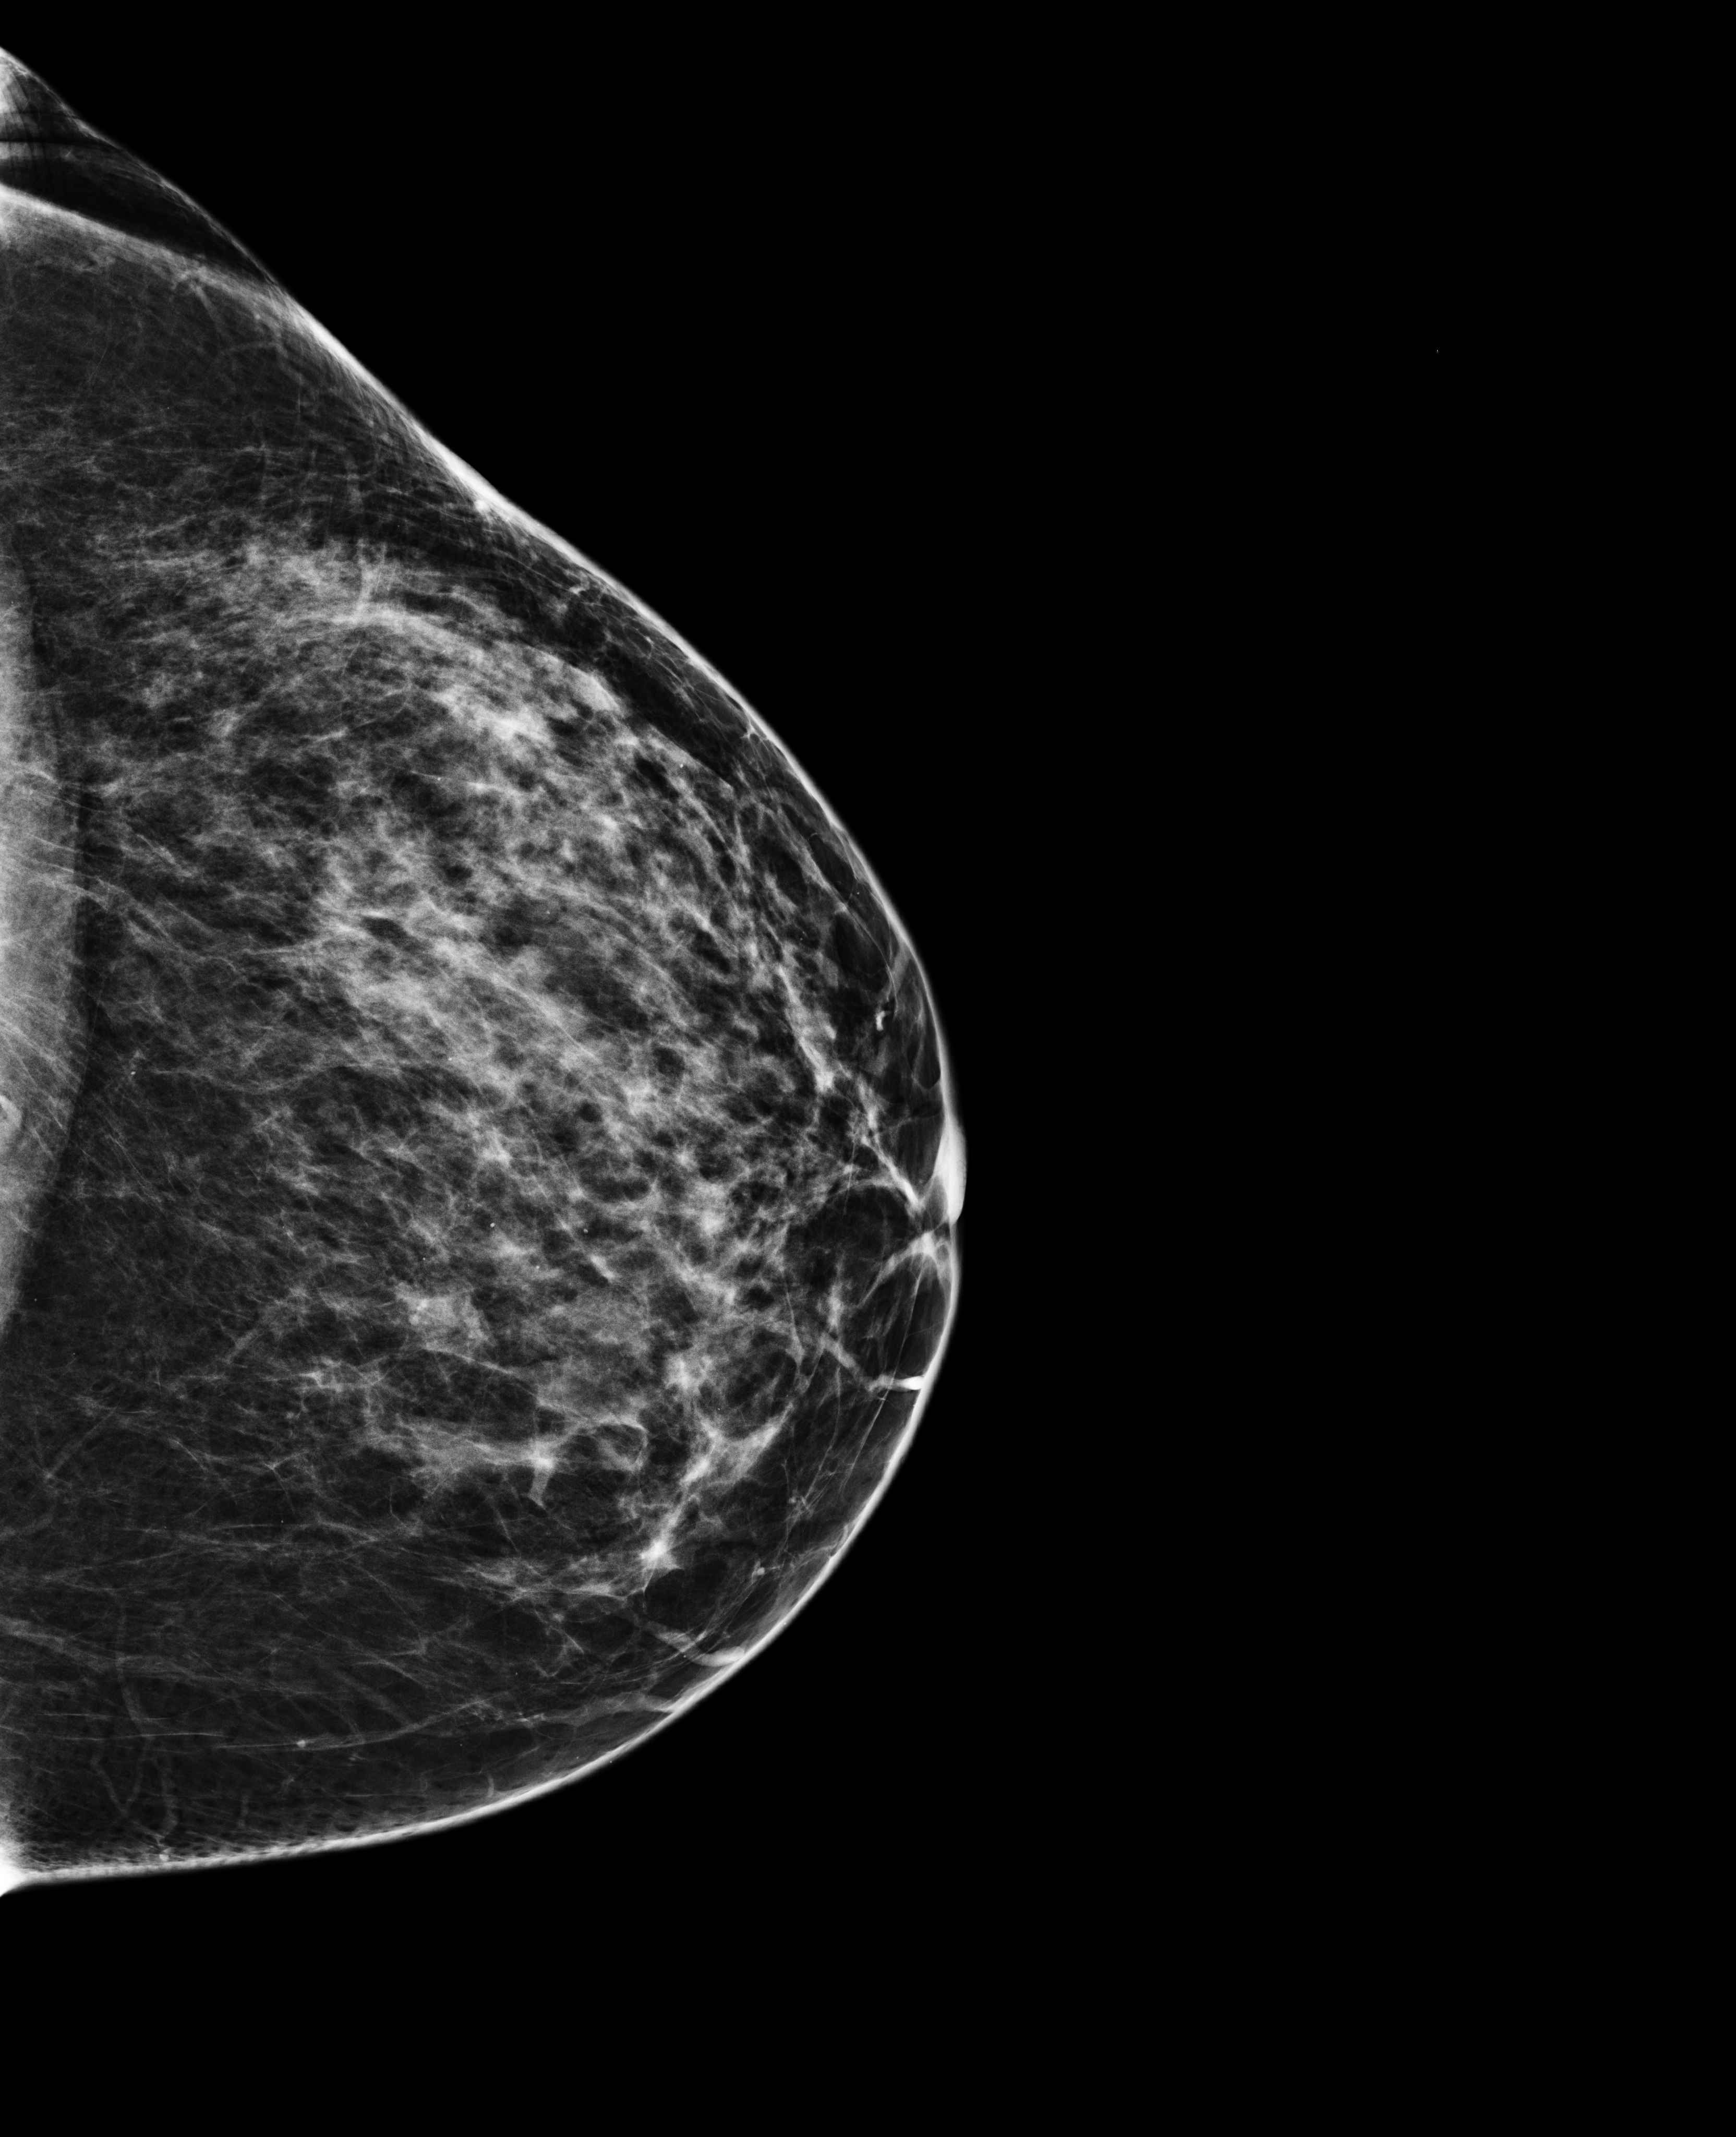
Full-field digital mammogram (FFDM), left breast, craniocaudal (CC) view, screening examination, compressed breast thickness 64 mm, system: Selenia Dimensions. Female patient, age 47 years.
- BI-RADS breast density category at the screening exam (both breasts, scale 1–4): 3
- final BI-RADS category for the screening round (tomosynthesis exam, both breasts): category 1
- recall: no recall after this screen